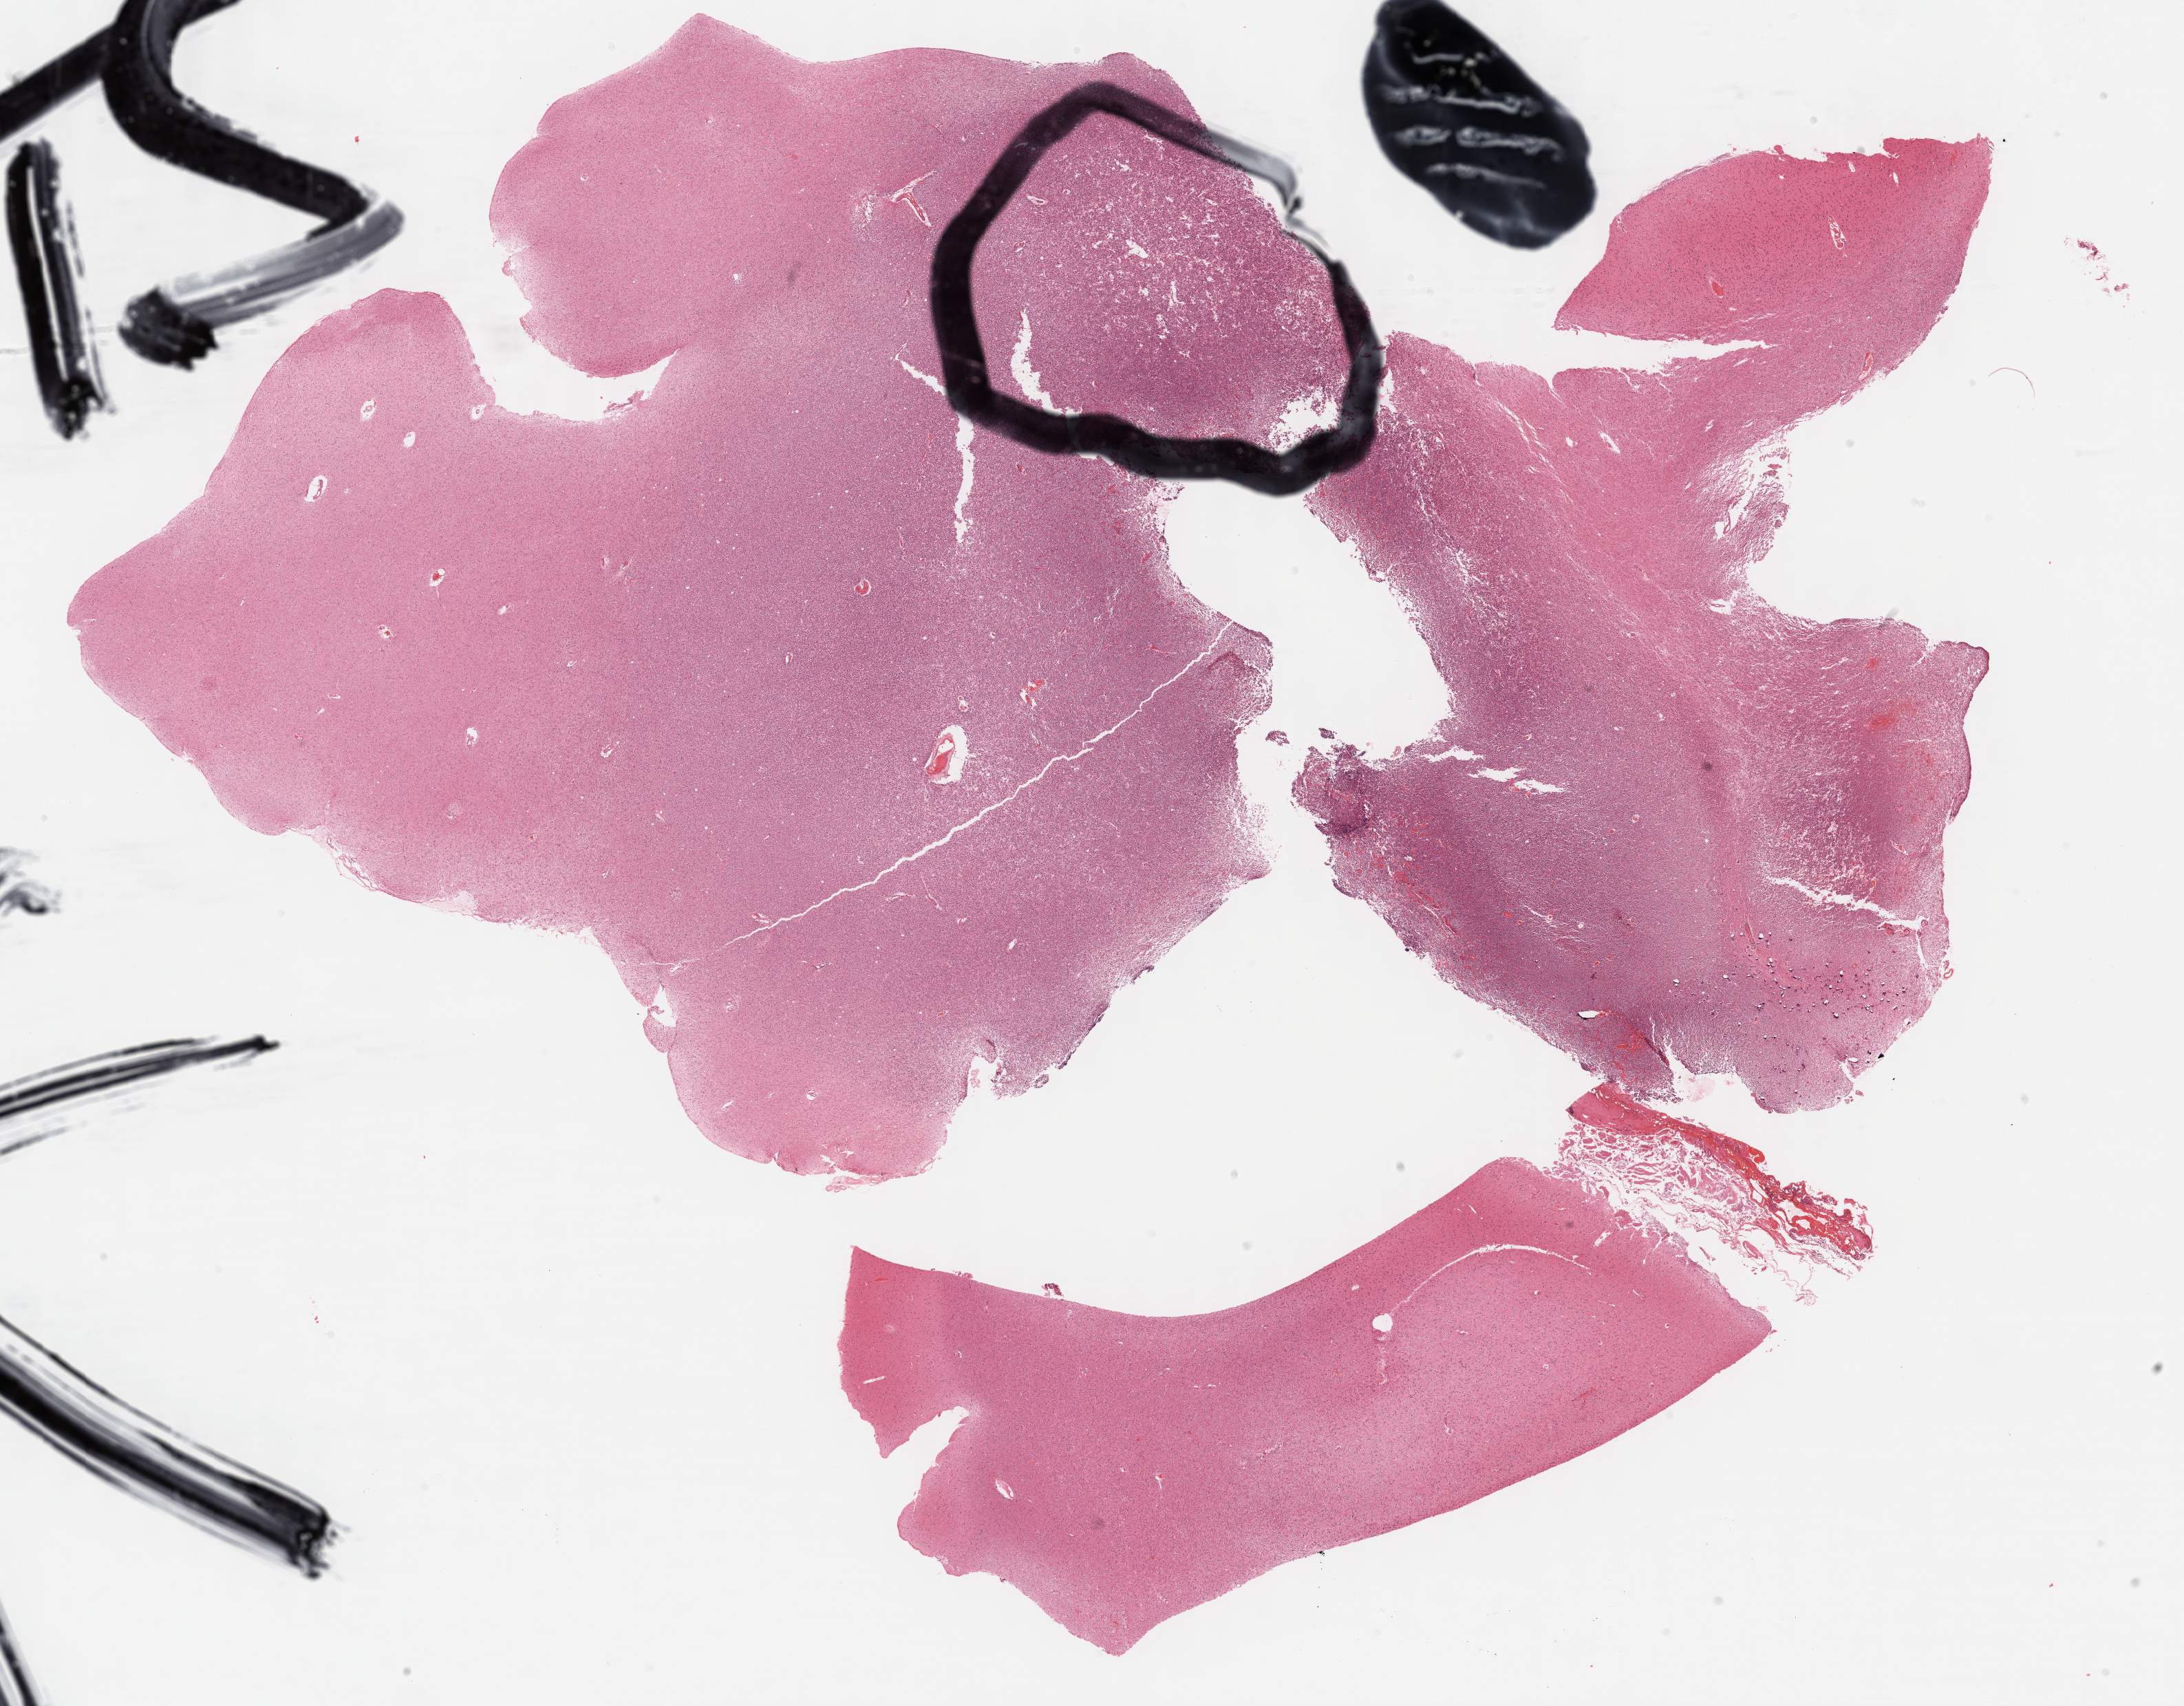
H&E-stained whole-slide image, whole scanned area (about 25.7 x 20.1 mm, slide scanned at 40x) shown as a low-resolution overview; formalin-fixed paraffin-embedded (FFPE) diagnostic section; sample: primary tumour, brain. Patient: female, age at initial diagnosis 54 years.
Diagnosis: Oligodendroglioma, anaplastic (cerebrum).